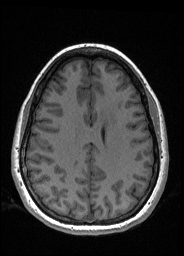
Pre-operative brain MRI before brain-tumour surgery, one axial slice; slice 70 of 176 in the series (ordered by position); T1-weighted post-contrast; 1 mm slice thickness; 184 × 256 image matrix, field of view 180 × 250 mm. Case-level facts recorded for this patient, not image findings: histopathology: Oligodendroglioma; WHO grade: 2; IDH mutation: yes; tumour location: Left Frontal.
Outlined on this slice (manually delineated by an expert):
- tumour: bounding box (x1, y1, x2, y2) in pixels: (100, 110, 114, 123)